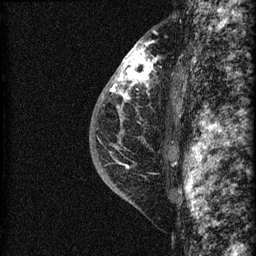
Breast MRI (dynamic contrast-enhanced), one sagittal slice; slice 43 of 60 in the series (ordered by position); dynamic contrast-enhanced series, image 2 of 3 at this slice position (ordered by acquisition); 1.5 T; TE 4.2 ms, TR 22.7 ms; 1.5 mm slice thickness; 256 × 256 image matrix, field of view 180 × 180 mm. Female patient, age 48 years. From the clinical record (not read from this slice): setting: breast cancer imaged before/during neoadjuvant chemotherapy; receptor status: triple-negative.
Structures marked on this image (semi-automatically segmented with operator editing):
- analysis volume of interest (the breast-tissue region the enhancement analysis was run in; not a lesion): box from (x=115, y=34) to (x=169, y=162) px
- tumour enhancement mask (voxels above the 90 % enhancement threshold inside the analysis volume of interest): (x=115, y=41)–(x=155, y=101)